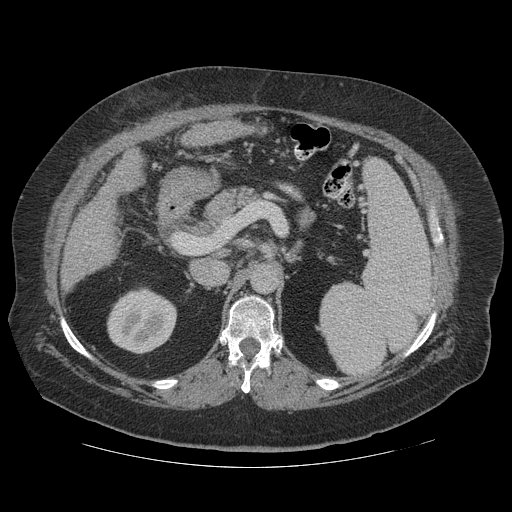
Contrast-enhanced abdominal CT (liver protocol), one axial slice; position 61 of 121 along the scan axis; reconstruction kernel STANDARD; soft-tissue window (W 400 / L 40 HU); 2.5 mm slice thickness; 512 × 512 image matrix, field of view 420 × 420 mm. Case-level facts recorded for this patient, not image findings: diagnosis: hepatocellular carcinoma (patient treated with transarterial chemoembolisation; whether this scan precedes or follows treatment is not stated here); TNM stage (as recorded): Stage-IIIA; Child-Pugh class: A; tumour nodularity: multinodular; tumour size: 7.4 cm.
Annotated regions visible in this slice (semi-automatically segmented with operator editing):
- liver parenchyma outside the tumour (the mass and vessels are separate outlines, so this box may not span the whole liver): bounding box [x1, y1, x2, y2] px = [62, 122, 245, 289]
- liver vessels: [85, 219, 90, 243]